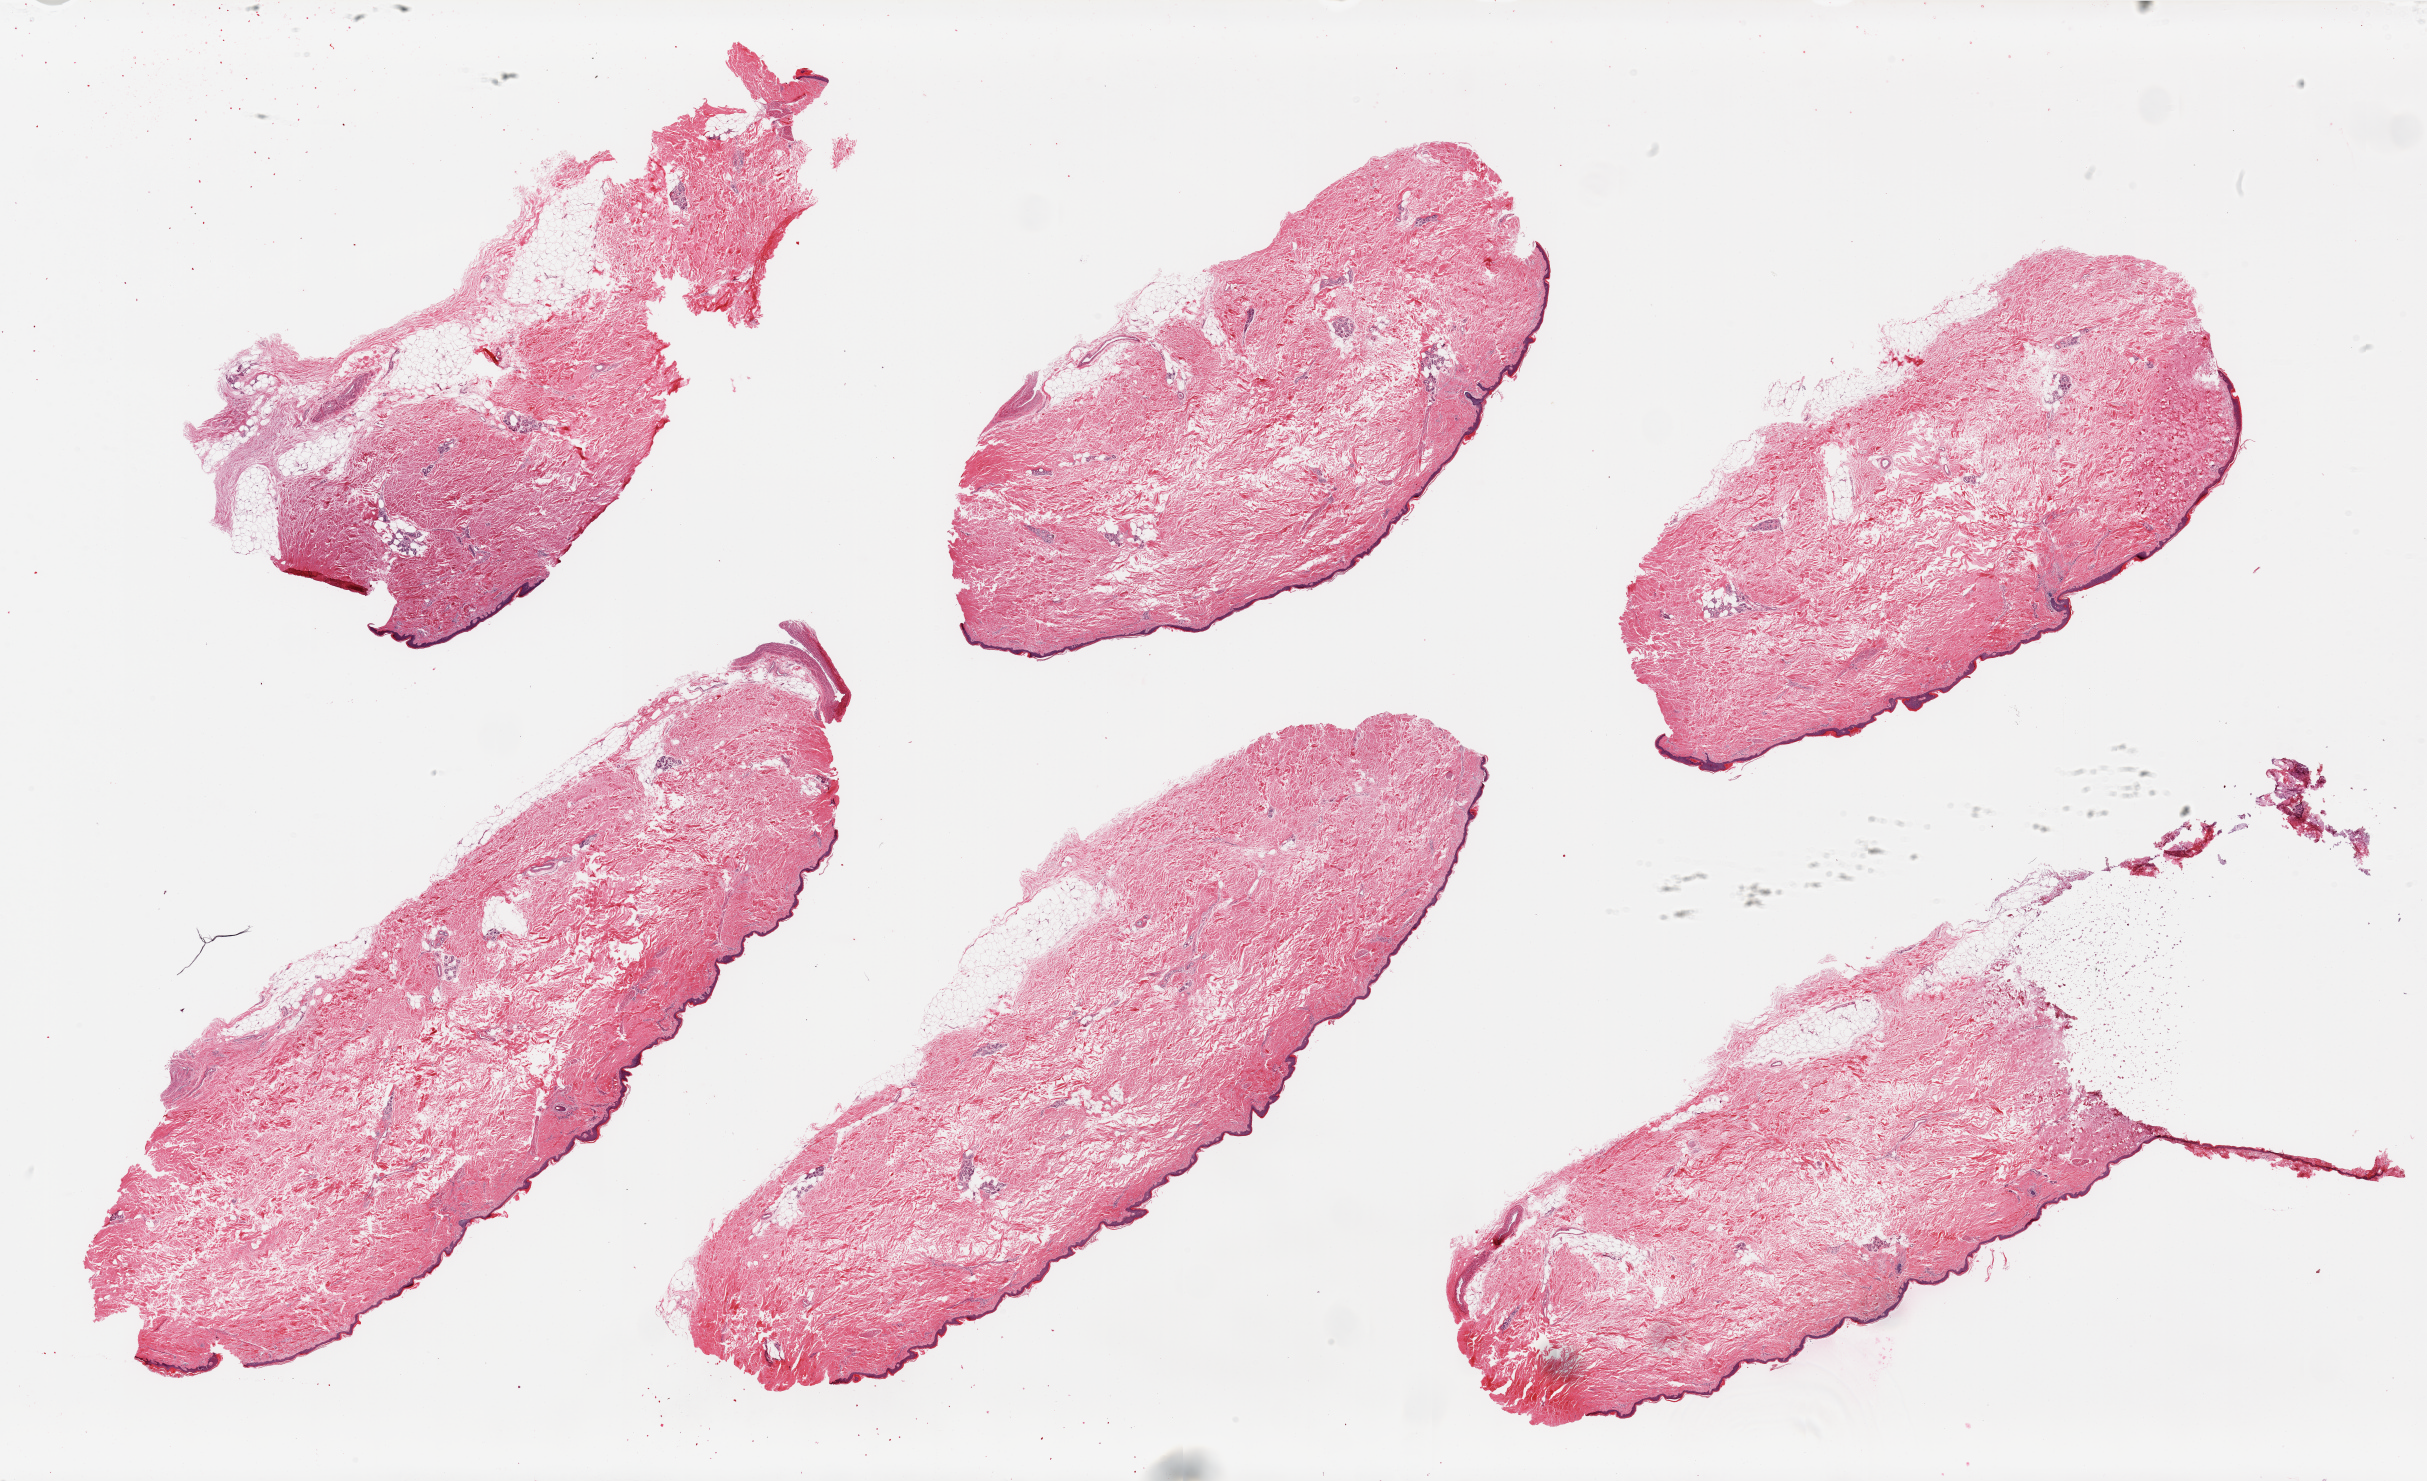
Digitized hematoxylin and eosin (H&E)-stained section, whole scanned area (about 38.4 x 23.4 mm, slide scanned at 20x) shown as a low-resolution overview, PAXgene-fixed paraffin-embedded (PFPE) section, target tissue: skin of lower leg, tissue donor sample. Male donor.
Pathologist's review note for this sample: 6 pieces; 10% internal/external fat, epidermis ~ 37um in thickness.